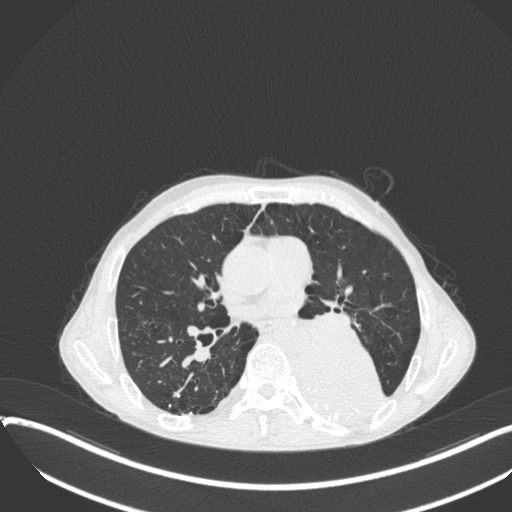
Chest CT, one axial slice; position 194 of 400 along the scan axis; reconstruction kernel B31f; lung window (W 1500 / L -600 HU); 1 mm slice thickness; 512 × 512 image matrix, field of view 400 × 400 mm. Male patient, age 57 years. Case-level facts recorded for this patient, not image findings: clinical TNM (as recorded): T4 N0 M0.
Structures marked on this image (bounding box drawn by a radiologist):
- lung tumour (recorded histology: squamous cell carcinoma): box from (x=287, y=334) to (x=389, y=427) px